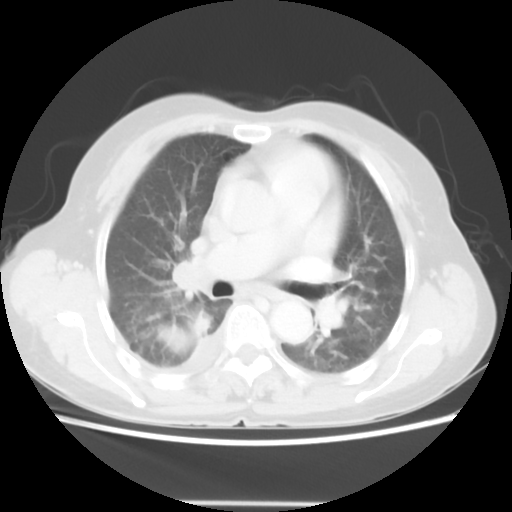
Chest CT, one axial slice. Slice 30 of 52 in the series (ordered by position). Lung window (W 1500 / L -600 HU). 5 mm slice thickness. 512 × 512 image matrix. Patient: female, 67 years. Case-level facts recorded for this patient, not image findings: clinical TNM (as recorded): T3 N1 M1.
Outlined on this slice (rectangle marked by the reading radiologist):
- lung tumour (recorded histology: adenocarcinoma): bounding box [x1, y1, x2, y2] px = [154, 308, 217, 356]